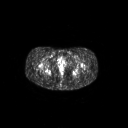
FDG PET of an extremity soft-tissue mass (from a PET/CT study), one axial slice; position 37 of 267 along the scan axis; 128 × 128 image matrix. Female patient, age 17 years. From the clinical record (not read from this slice): histological type: epithelioid sarcoma; grade: intermediate; site of the primary tumour: right buttock.
Structures marked on this image (expert contour drawn on MRI and transferred to this co-registered scan by the dataset authors):
- gross tumour volume including surrounding oedema: box from (x=52, y=71) to (x=56, y=76) px